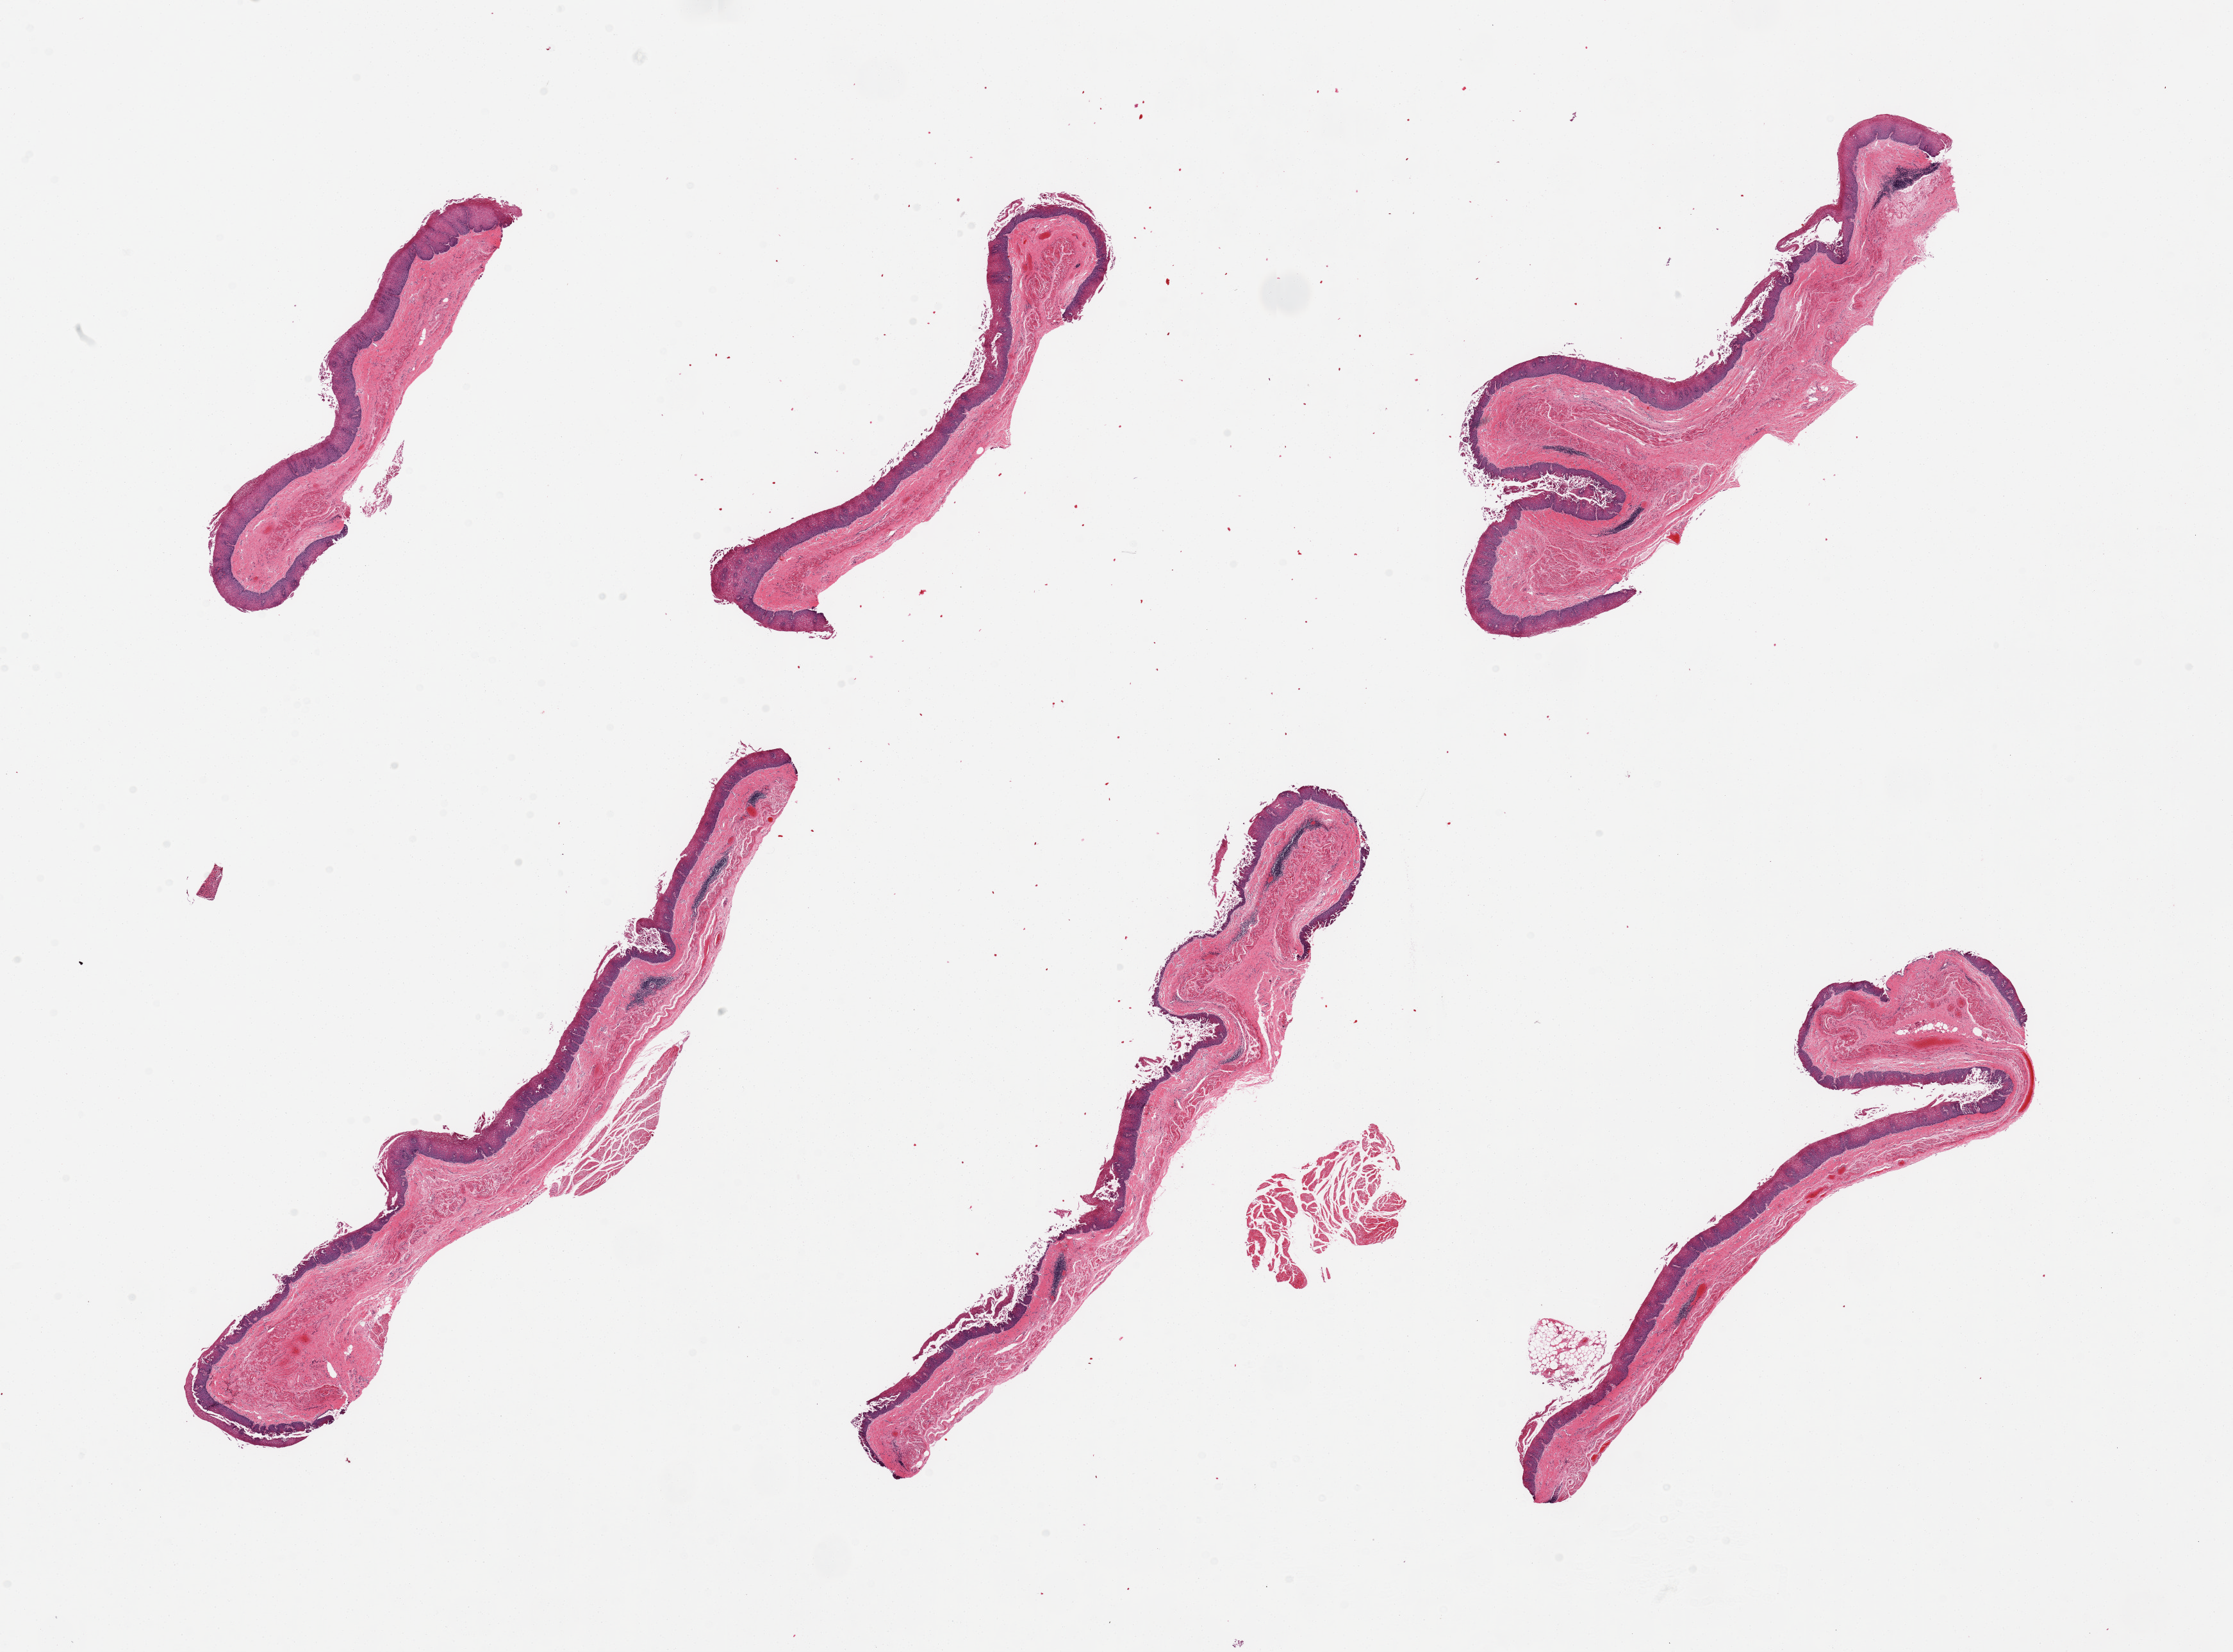
Digitized H&E-stained section, brightfield — whole scanned area (about 27.6 x 20.4 mm) shown as a low-resolution overview, PAXgene-fixed, paraffin-embedded tissue, section of esophageal mucous membrane (target tissue), tissue donor sample.
Review note (as recorded): 6 pieces, predominantly mucosa with few detached fragments of muscularis and fat, squamous epithelium sloughing, few collections of lymphocytes.